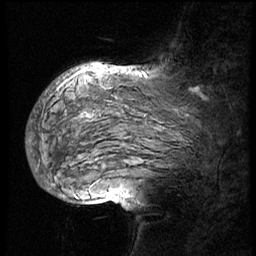
Breast MRI (dynamic contrast-enhanced), one sagittal slice. Position 39 of 56 along the scan axis. 3 images stored at this slice position (order not interpretable as contrast timing). 1.5 T. TE 4.2 ms, TR 8.9 ms. 3 mm slice thickness. 256 × 256 image matrix, field of view 220 × 220 mm. Female patient, age 57 years. Case-level facts recorded for this patient, not image findings: setting: breast cancer imaged before/during neoadjuvant chemotherapy; receptor status: HER2-positive.
Annotated regions visible in this slice (semi-automatically segmented with operator editing):
- analysis volume of interest (the breast-tissue region the enhancement analysis was run in; not a lesion): bounding box [x1, y1, x2, y2] px = [28, 70, 228, 156]
- tumour enhancement mask (voxels above the 140 % enhancement threshold inside the analysis volume of interest): [65, 70, 198, 91]